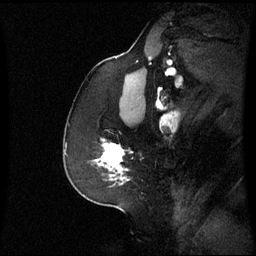
Breast MRI (dynamic contrast-enhanced), one sagittal slice; position 42 of 60 along the scan axis; dynamic contrast-enhanced series, image 2 of 3 at this slice position (ordered by acquisition); 1.5 T; TE 4.2 ms, TR 8.9 ms; 2.4 mm slice thickness; 256 × 256 image matrix, field of view 230 × 230 mm. Patient: female, 59 years. Case-level facts recorded for this patient, not image findings: setting: breast cancer imaged before/during neoadjuvant chemotherapy; receptor status: triple-negative.
Structures marked on this image (semi-automatically segmented with operator editing):
- analysis volume of interest (the breast-tissue region the enhancement analysis was run in; not a lesion): bounding box <96,139,130,183> (left, top, right, bottom; pixels)
- tumour enhancement mask (voxels above the 70 % enhancement threshold inside the analysis volume of interest): <97,139,125,179>